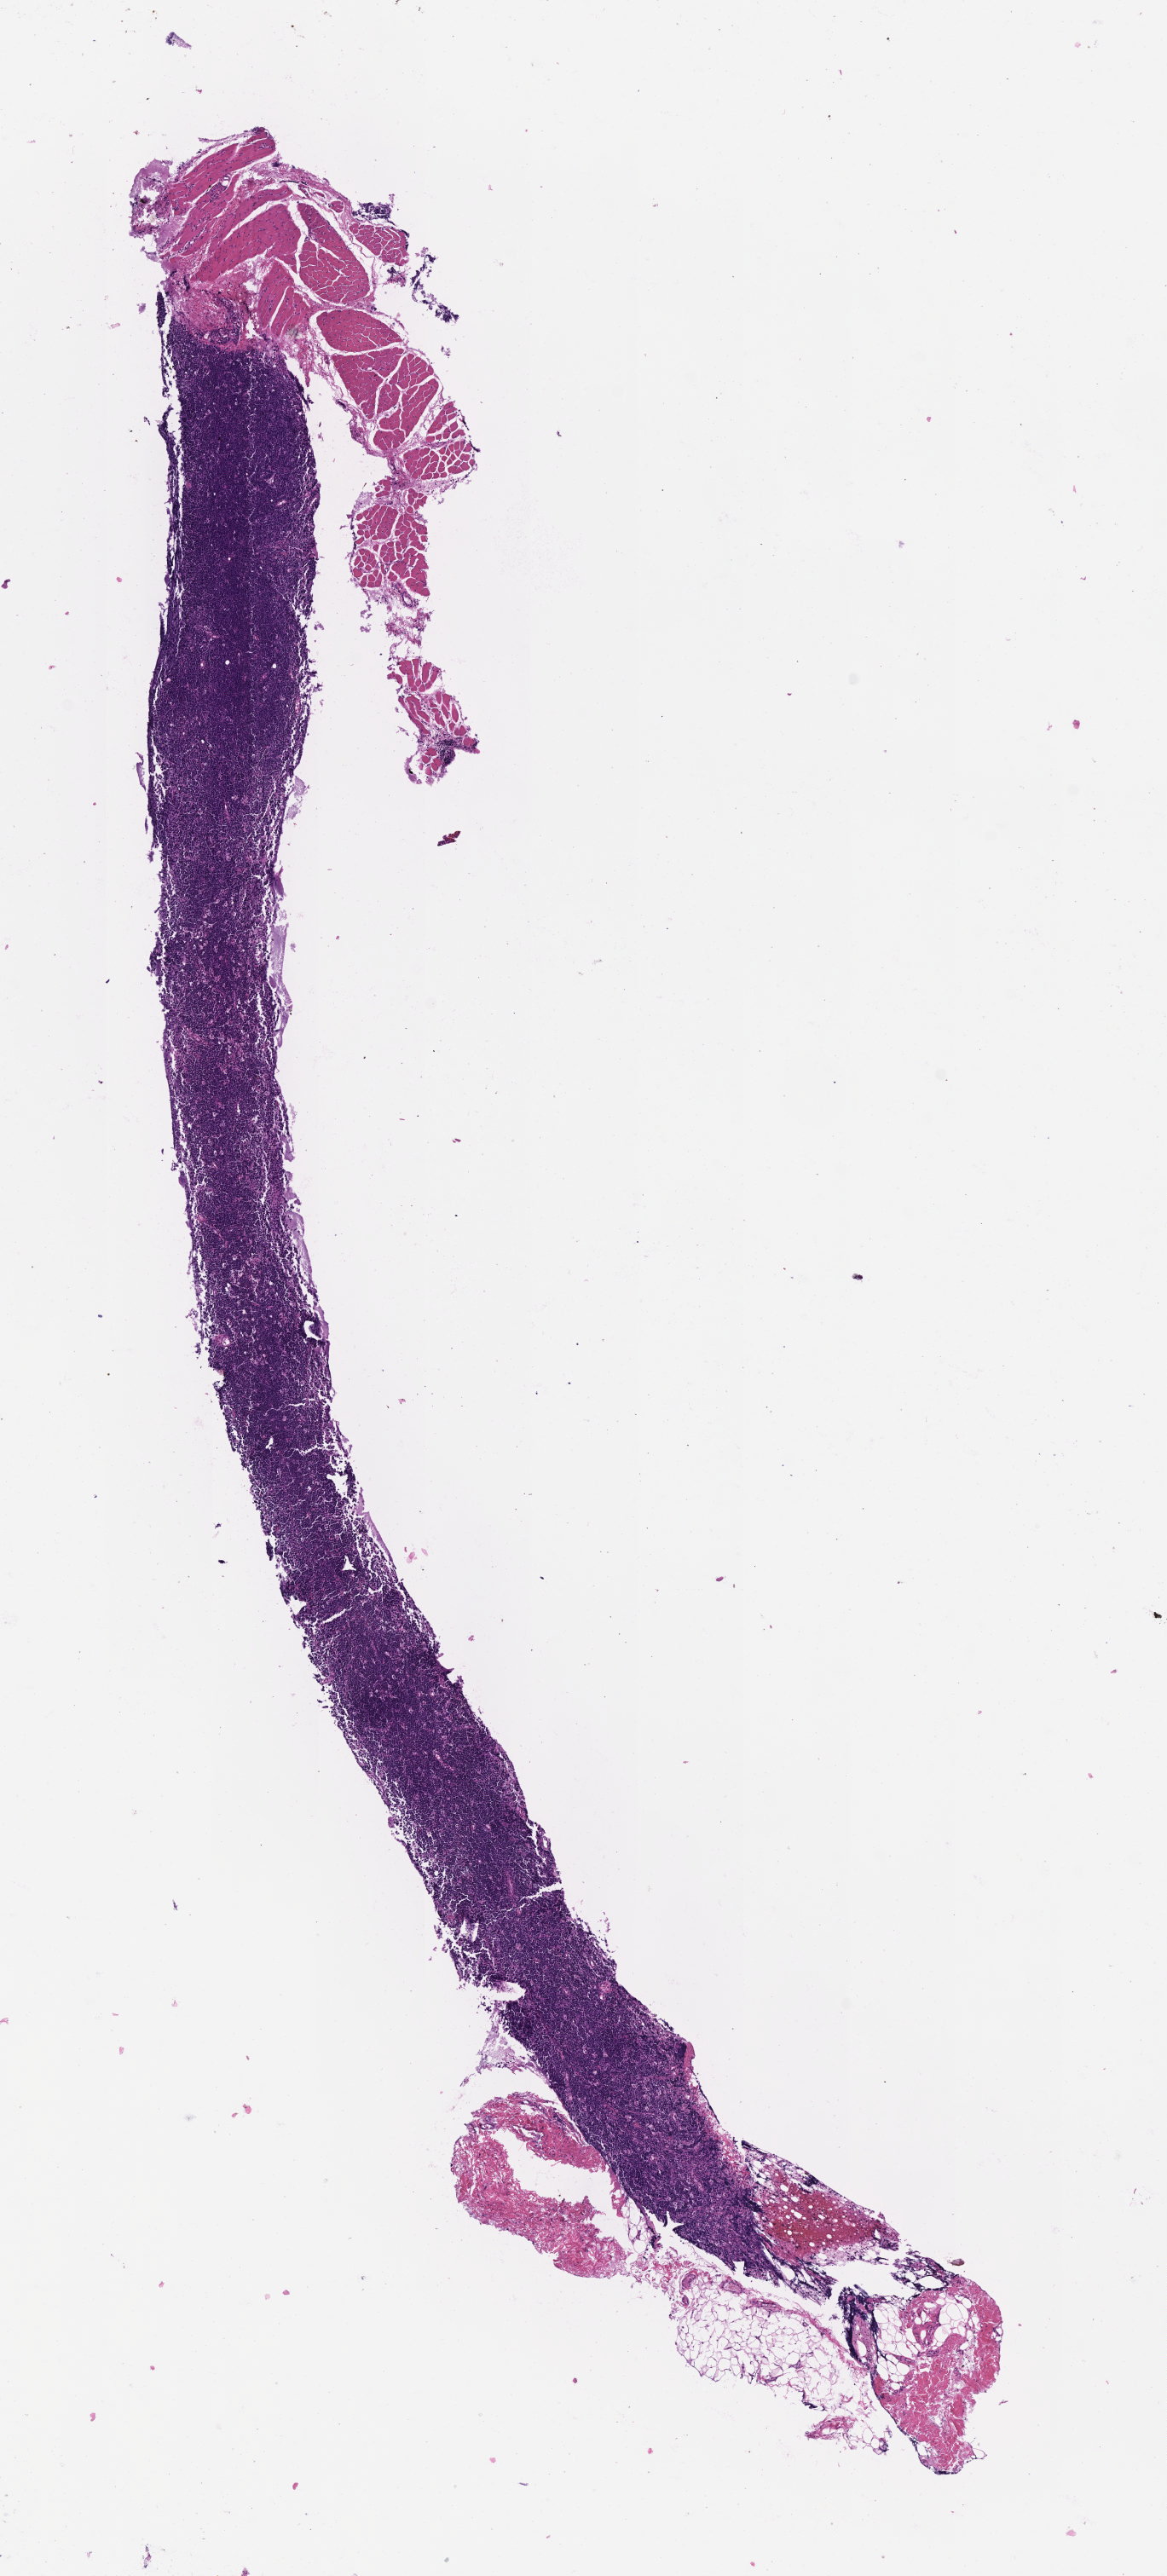
Hematoxylin and eosin (H&E) whole-slide image — a low-resolution overview of the entire scanned area, about 5.5 x 12.2 mm, tumor tissue, site: cranium. Patient: female, age at initial diagnosis 7 years.
Diagnosis: Burkitt lymphoma, NOS.